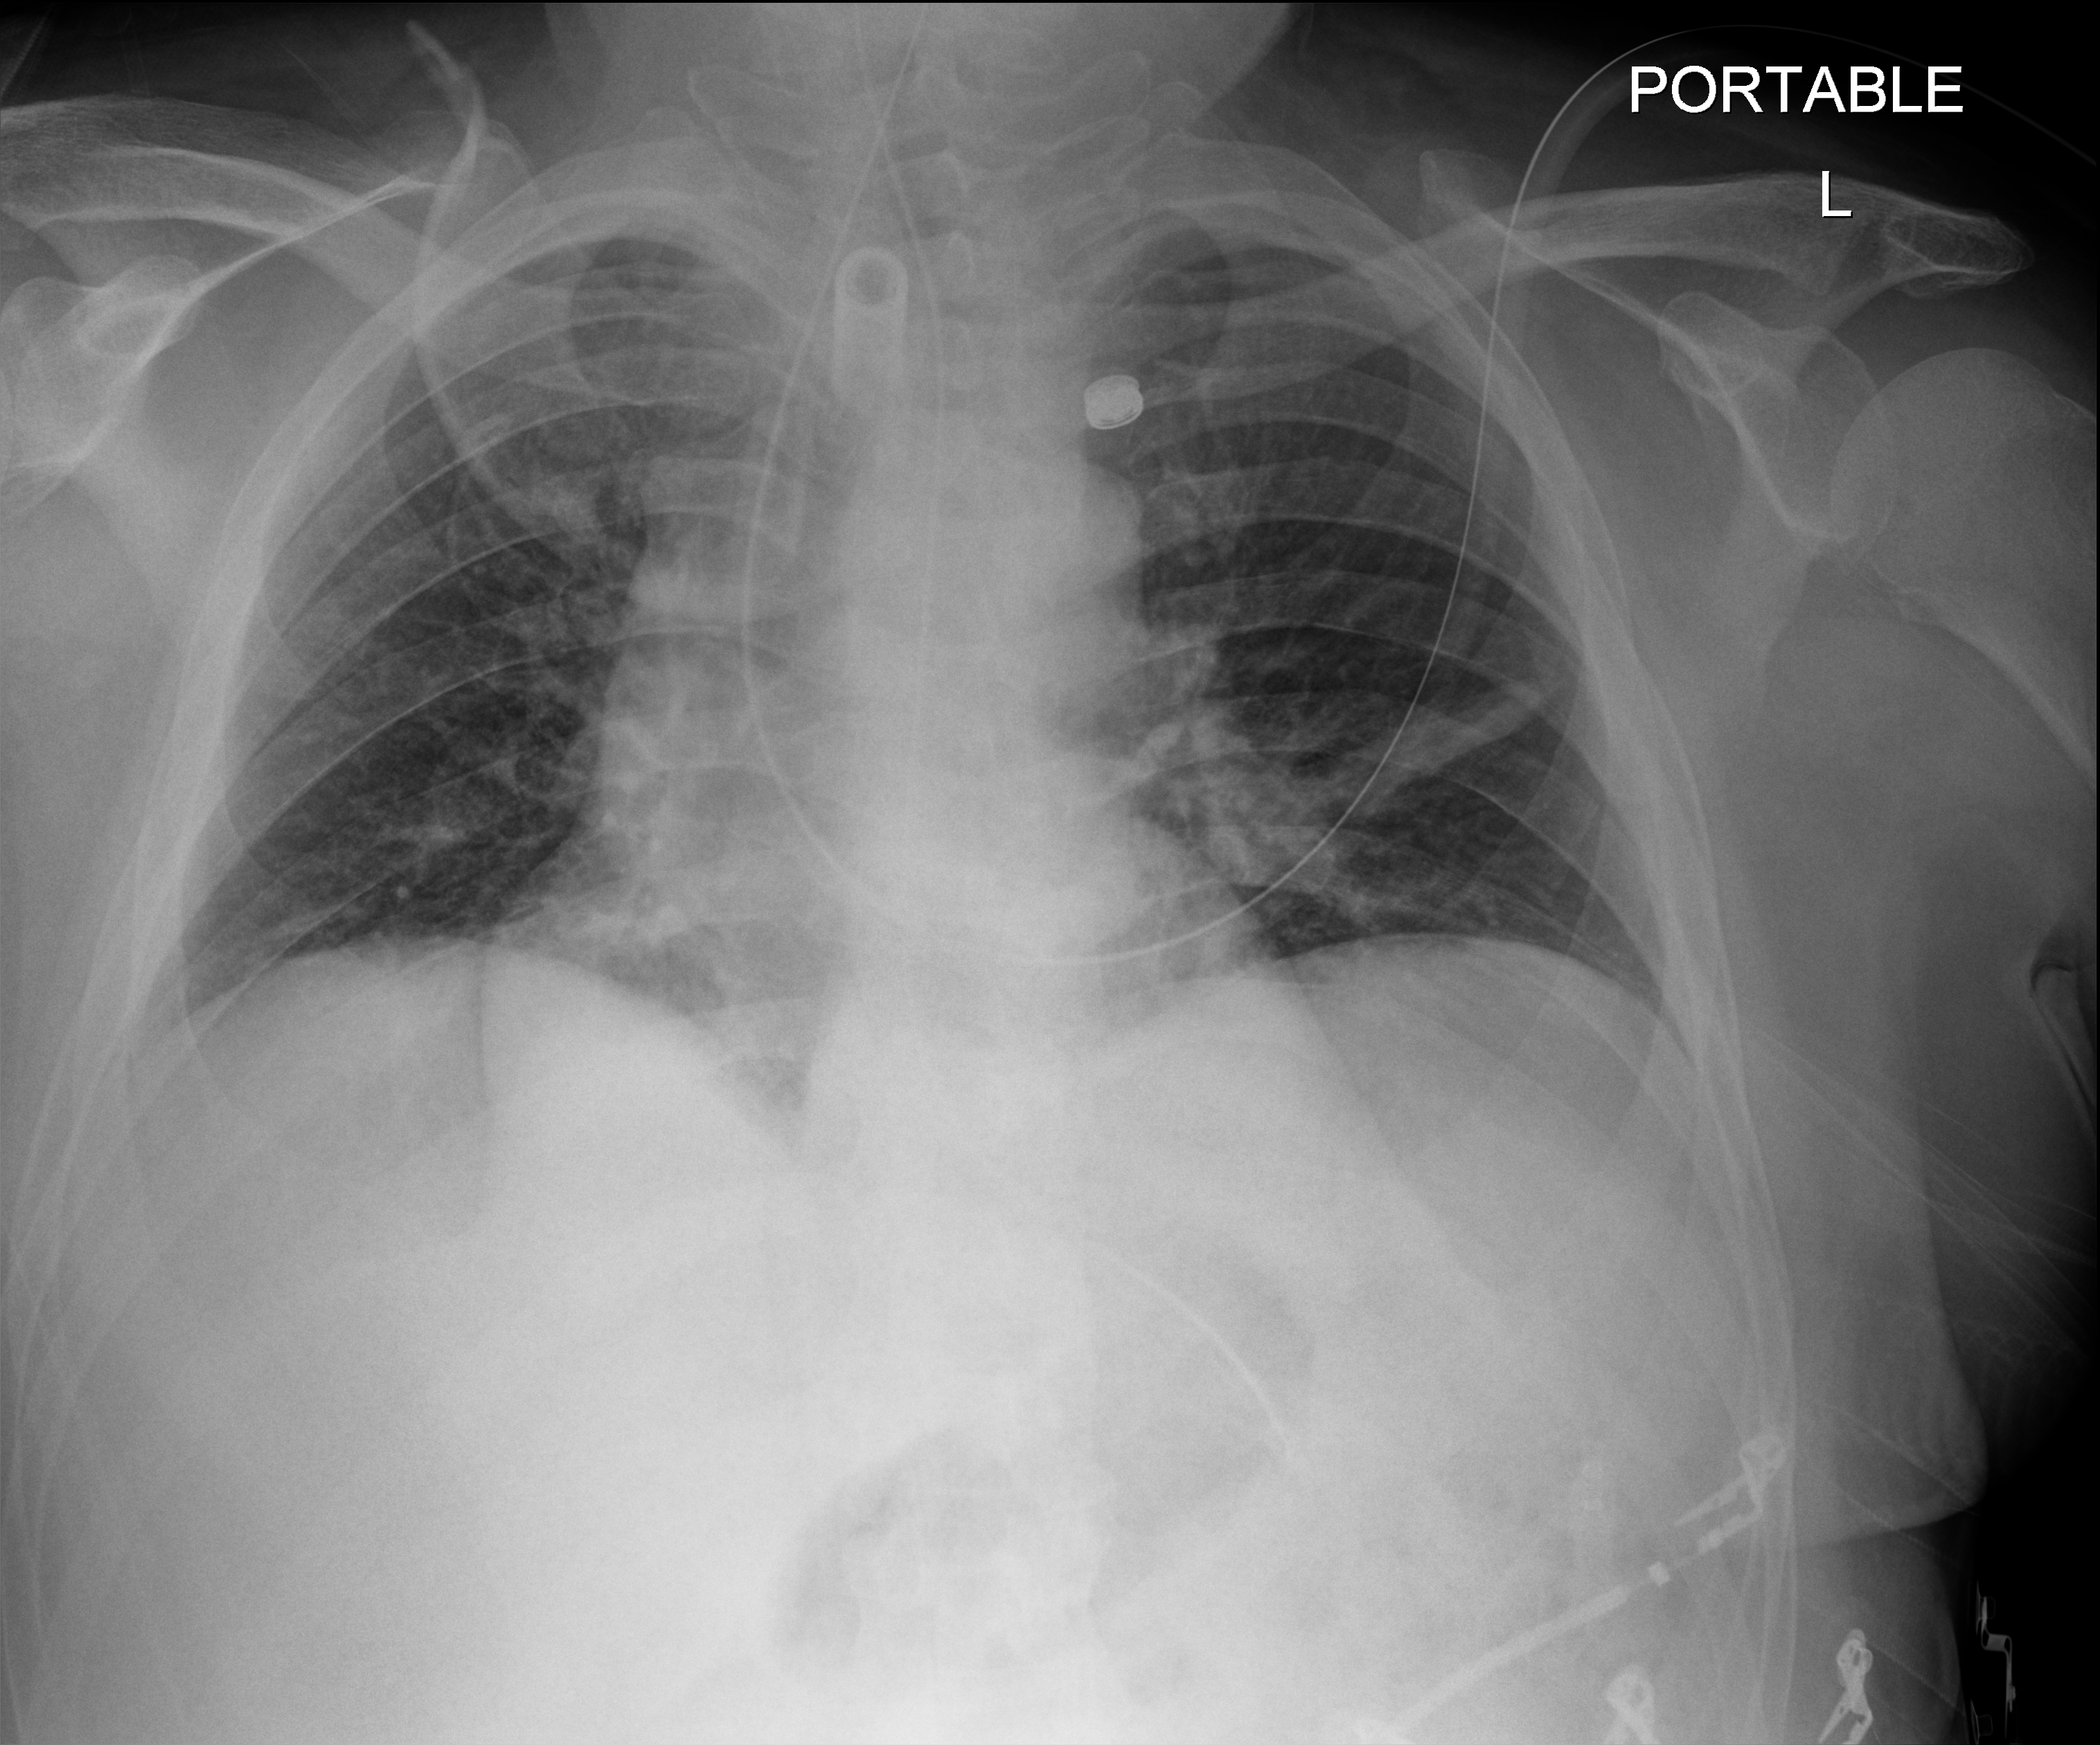
Portable chest radiograph, anteroposterior (AP) projection. Male patient hospitalised with COVID-19, age 18–59 years.
Hospital-stay facts (about this admission, not read from this image; timing relative to this image not recorded):
- admitted to intensive care during this hospital stay: yes
- mechanically ventilated during this hospital stay: yes